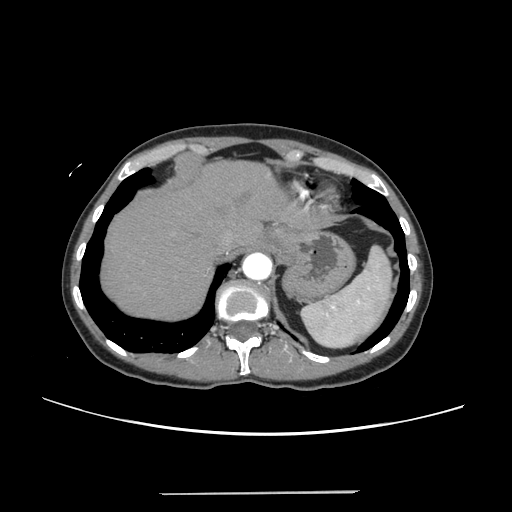
Contrast-enhanced abdominal CT, one axial slice; slice 204 of 240 in the series (ordered by position); intravenous contrast given; soft-tissue window (W 400 / L 40 HU); 1.25 mm slice thickness; 512 × 512 image matrix, field of view 371 × 371 mm. Female patient, age 60 years. From the clinical record (not read from this slice): diagnosis: colorectal cancer liver metastases, imaged before liver resection; multiple liver metastases: no; largest metastasis: 1.5 cm; disease in both lobes: no.
Outlined on this slice (manually delineated by an expert):
- hepatic veins: box from (x=221, y=223) to (x=250, y=250) px
- liver: (x=102, y=162)–(x=313, y=318)
- planned liver remnant (the part of the liver to remain after resection): (x=102, y=161)–(x=307, y=318)